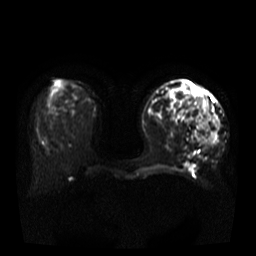
Breast MRI, one axial slice; diffusion-weighted series; image 2 of 4 stored at this slice position (different b-values; order by instance number); 3 T; 5 mm slice thickness; 256 × 256 image matrix, field of view 380 × 380 mm. Female patient.
Outlined on this slice (outlined manually by an expert reader):
- tumour on diffusion-weighted imaging: bounding box [x1, y1, x2, y2] px = [194, 98, 219, 146]